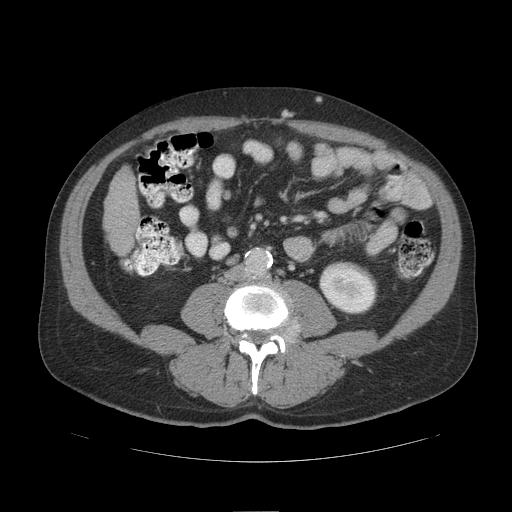
Contrast-enhanced abdominal CT (liver protocol), one axial slice. Position 24 of 109 along the scan axis. Reconstruction kernel STANDARD. 140 kVp. Soft-tissue window (W 400 / L 40 HU). 2.5 mm slice thickness. 512 × 512 image matrix. Case-level facts recorded for this patient, not image findings: diagnosis: hepatocellular carcinoma (patient treated with transarterial chemoembolisation; whether this scan precedes or follows treatment is not stated here); TNM stage (as recorded): Stage-IIIB; Child-Pugh class: A; tumour differentiation: poorly differentiated; tumour nodularity: multinodular.
Annotated regions visible in this slice (semi-automatically segmented with operator editing):
- liver parenchyma outside the tumour (the mass and vessels are separate outlines, so this box may not span the whole liver): bounding box <104,168,138,254> (left, top, right, bottom; pixels)